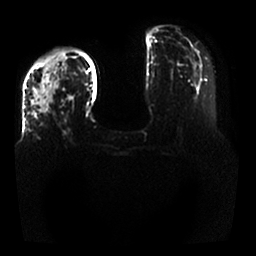
Breast MRI, one axial slice; slice 11 of 25 in the series (ordered by position); diffusion-weighted series; image 2 of 4 stored at this slice position (different b-values; order by instance number); 1.5 T; 256 × 256 image matrix, field of view 350 × 350 mm. Female patient.
Structures marked on this image (expert manual segmentation):
- tumour on diffusion-weighted imaging: box from (x=33, y=57) to (x=58, y=113) px